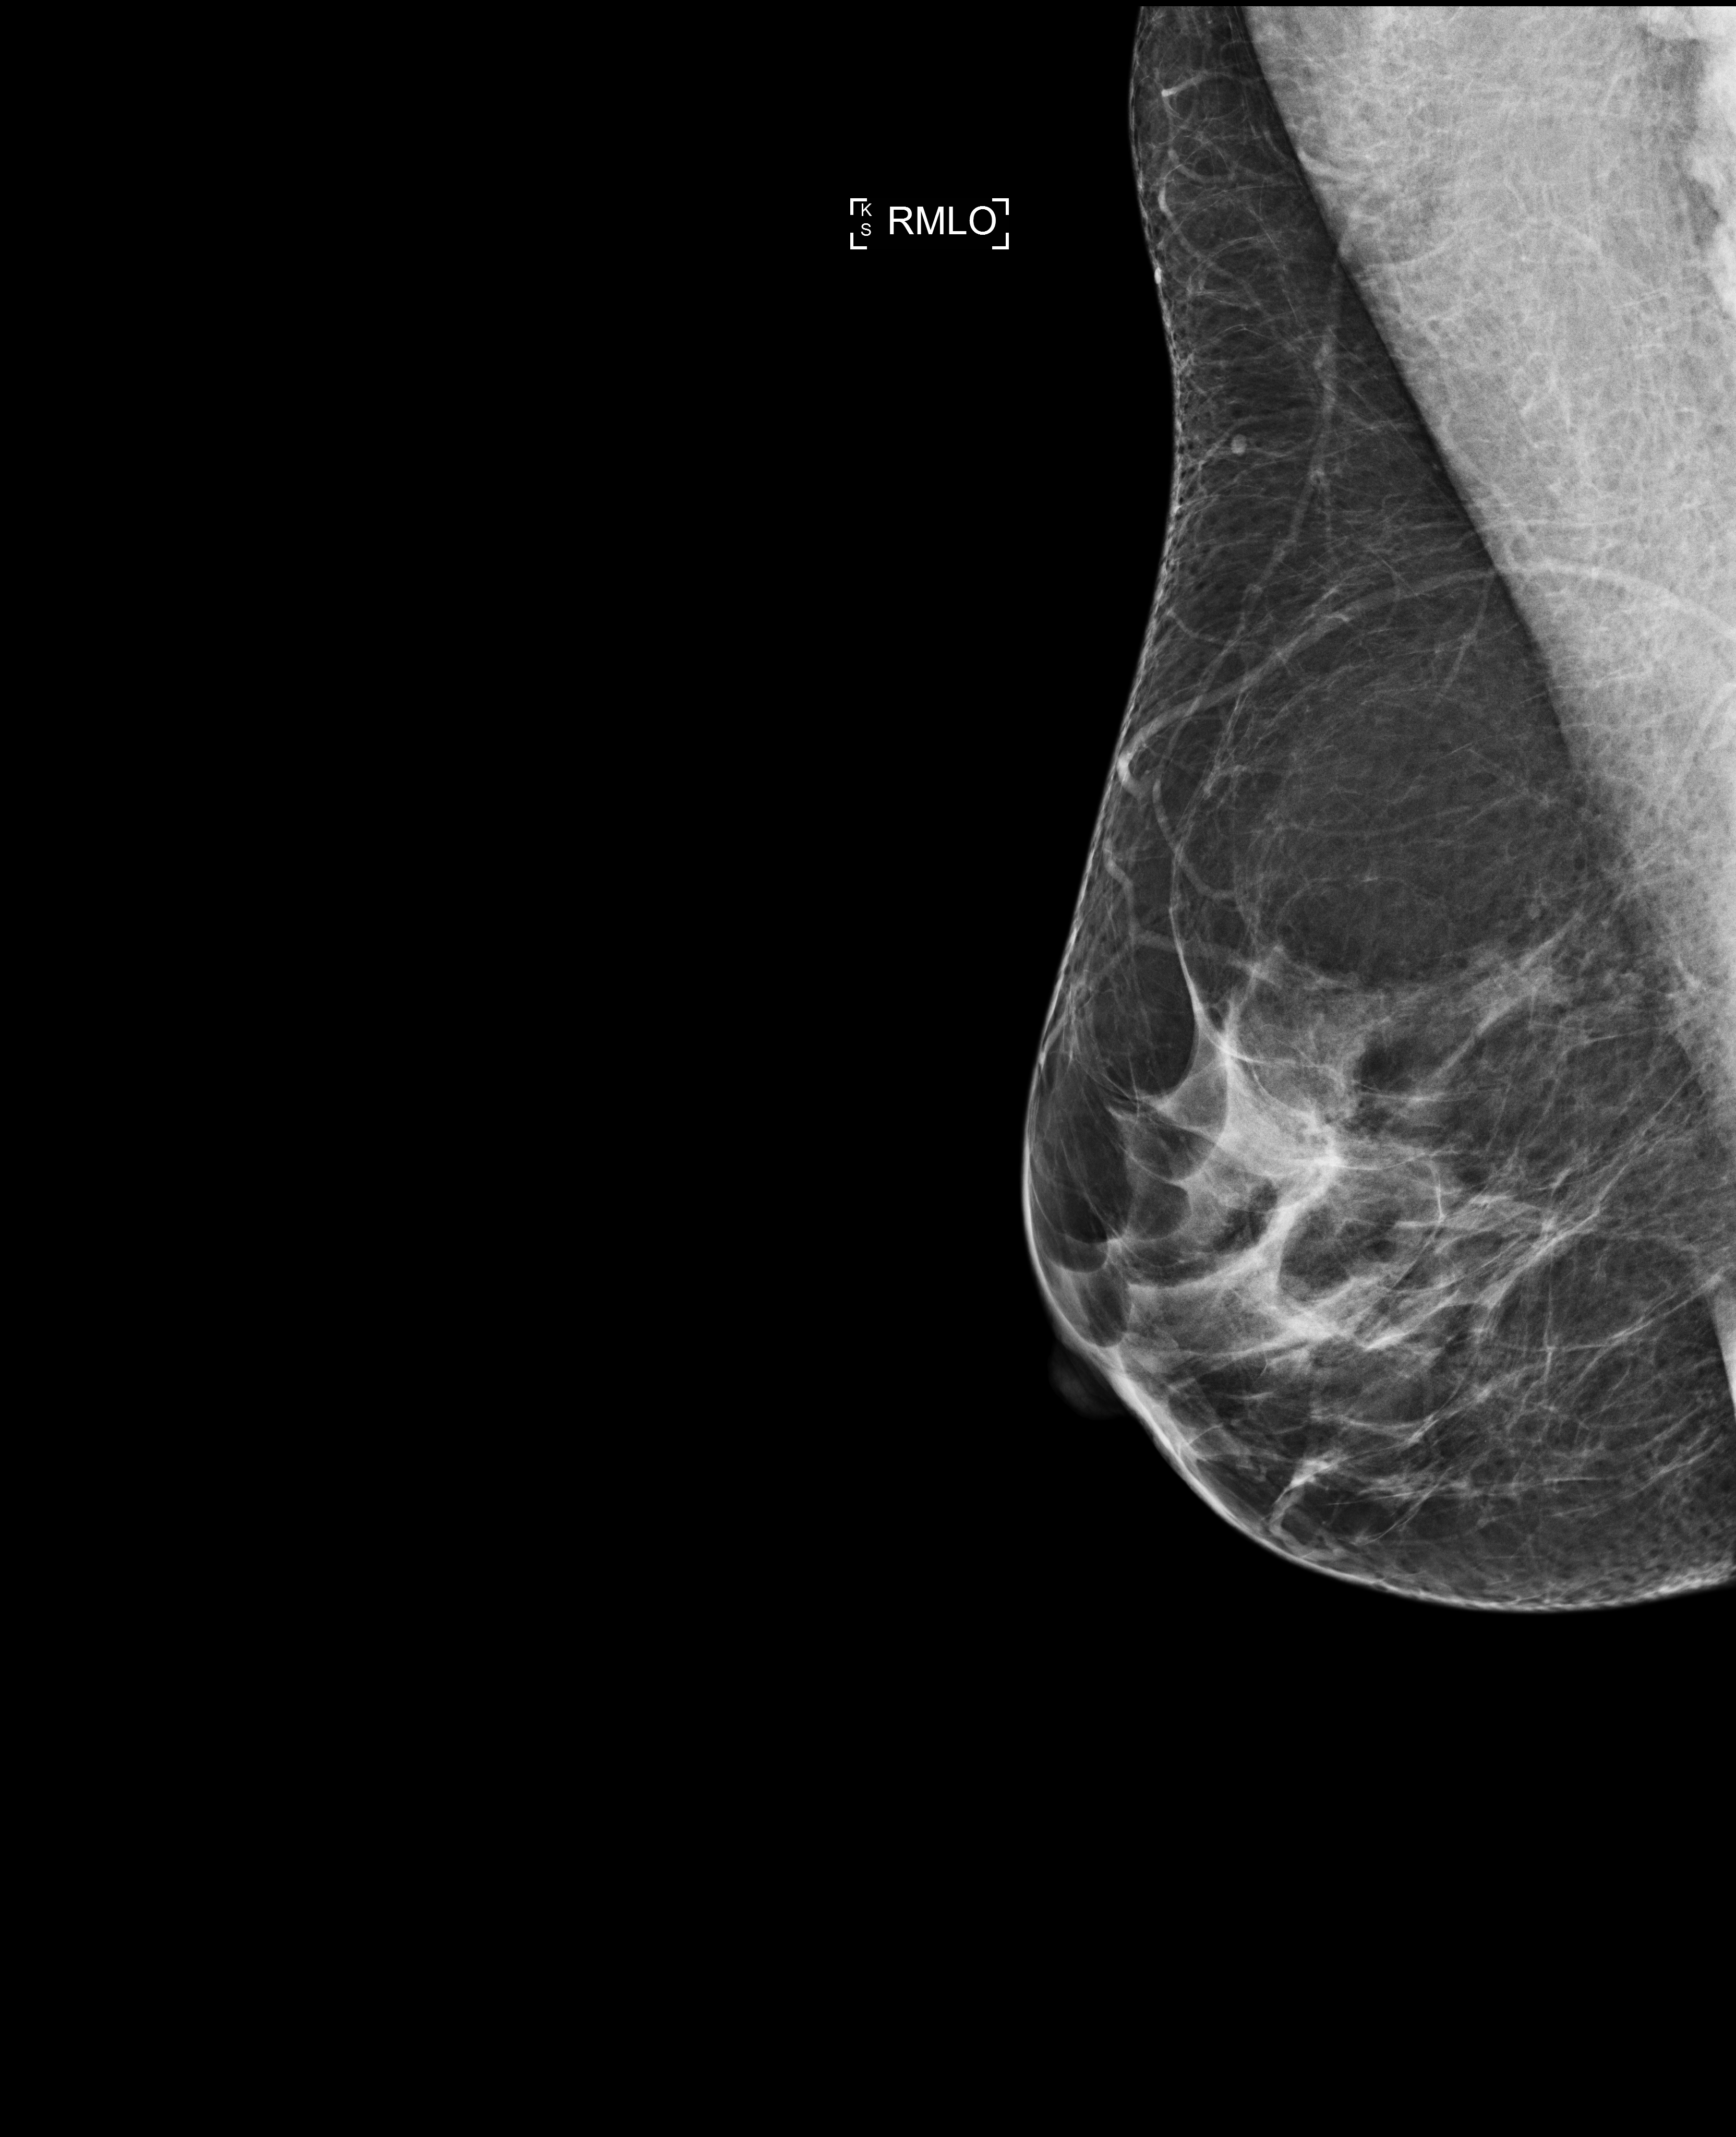
Digital mammogram (FFDM); right breast; medio-lateral oblique projection; diagnostic work-up study; compressed breast thickness 63 mm; system: Selenia Dimensions. Patient aged 49 years (female).
BI-RADS breast density category at the screening exam (both breasts, scale 1–4): 3. Final BI-RADS assessment for this screening round (tomosynthesis exam, both breasts): category 2. Recall: recalled for additional imaging after this screen.